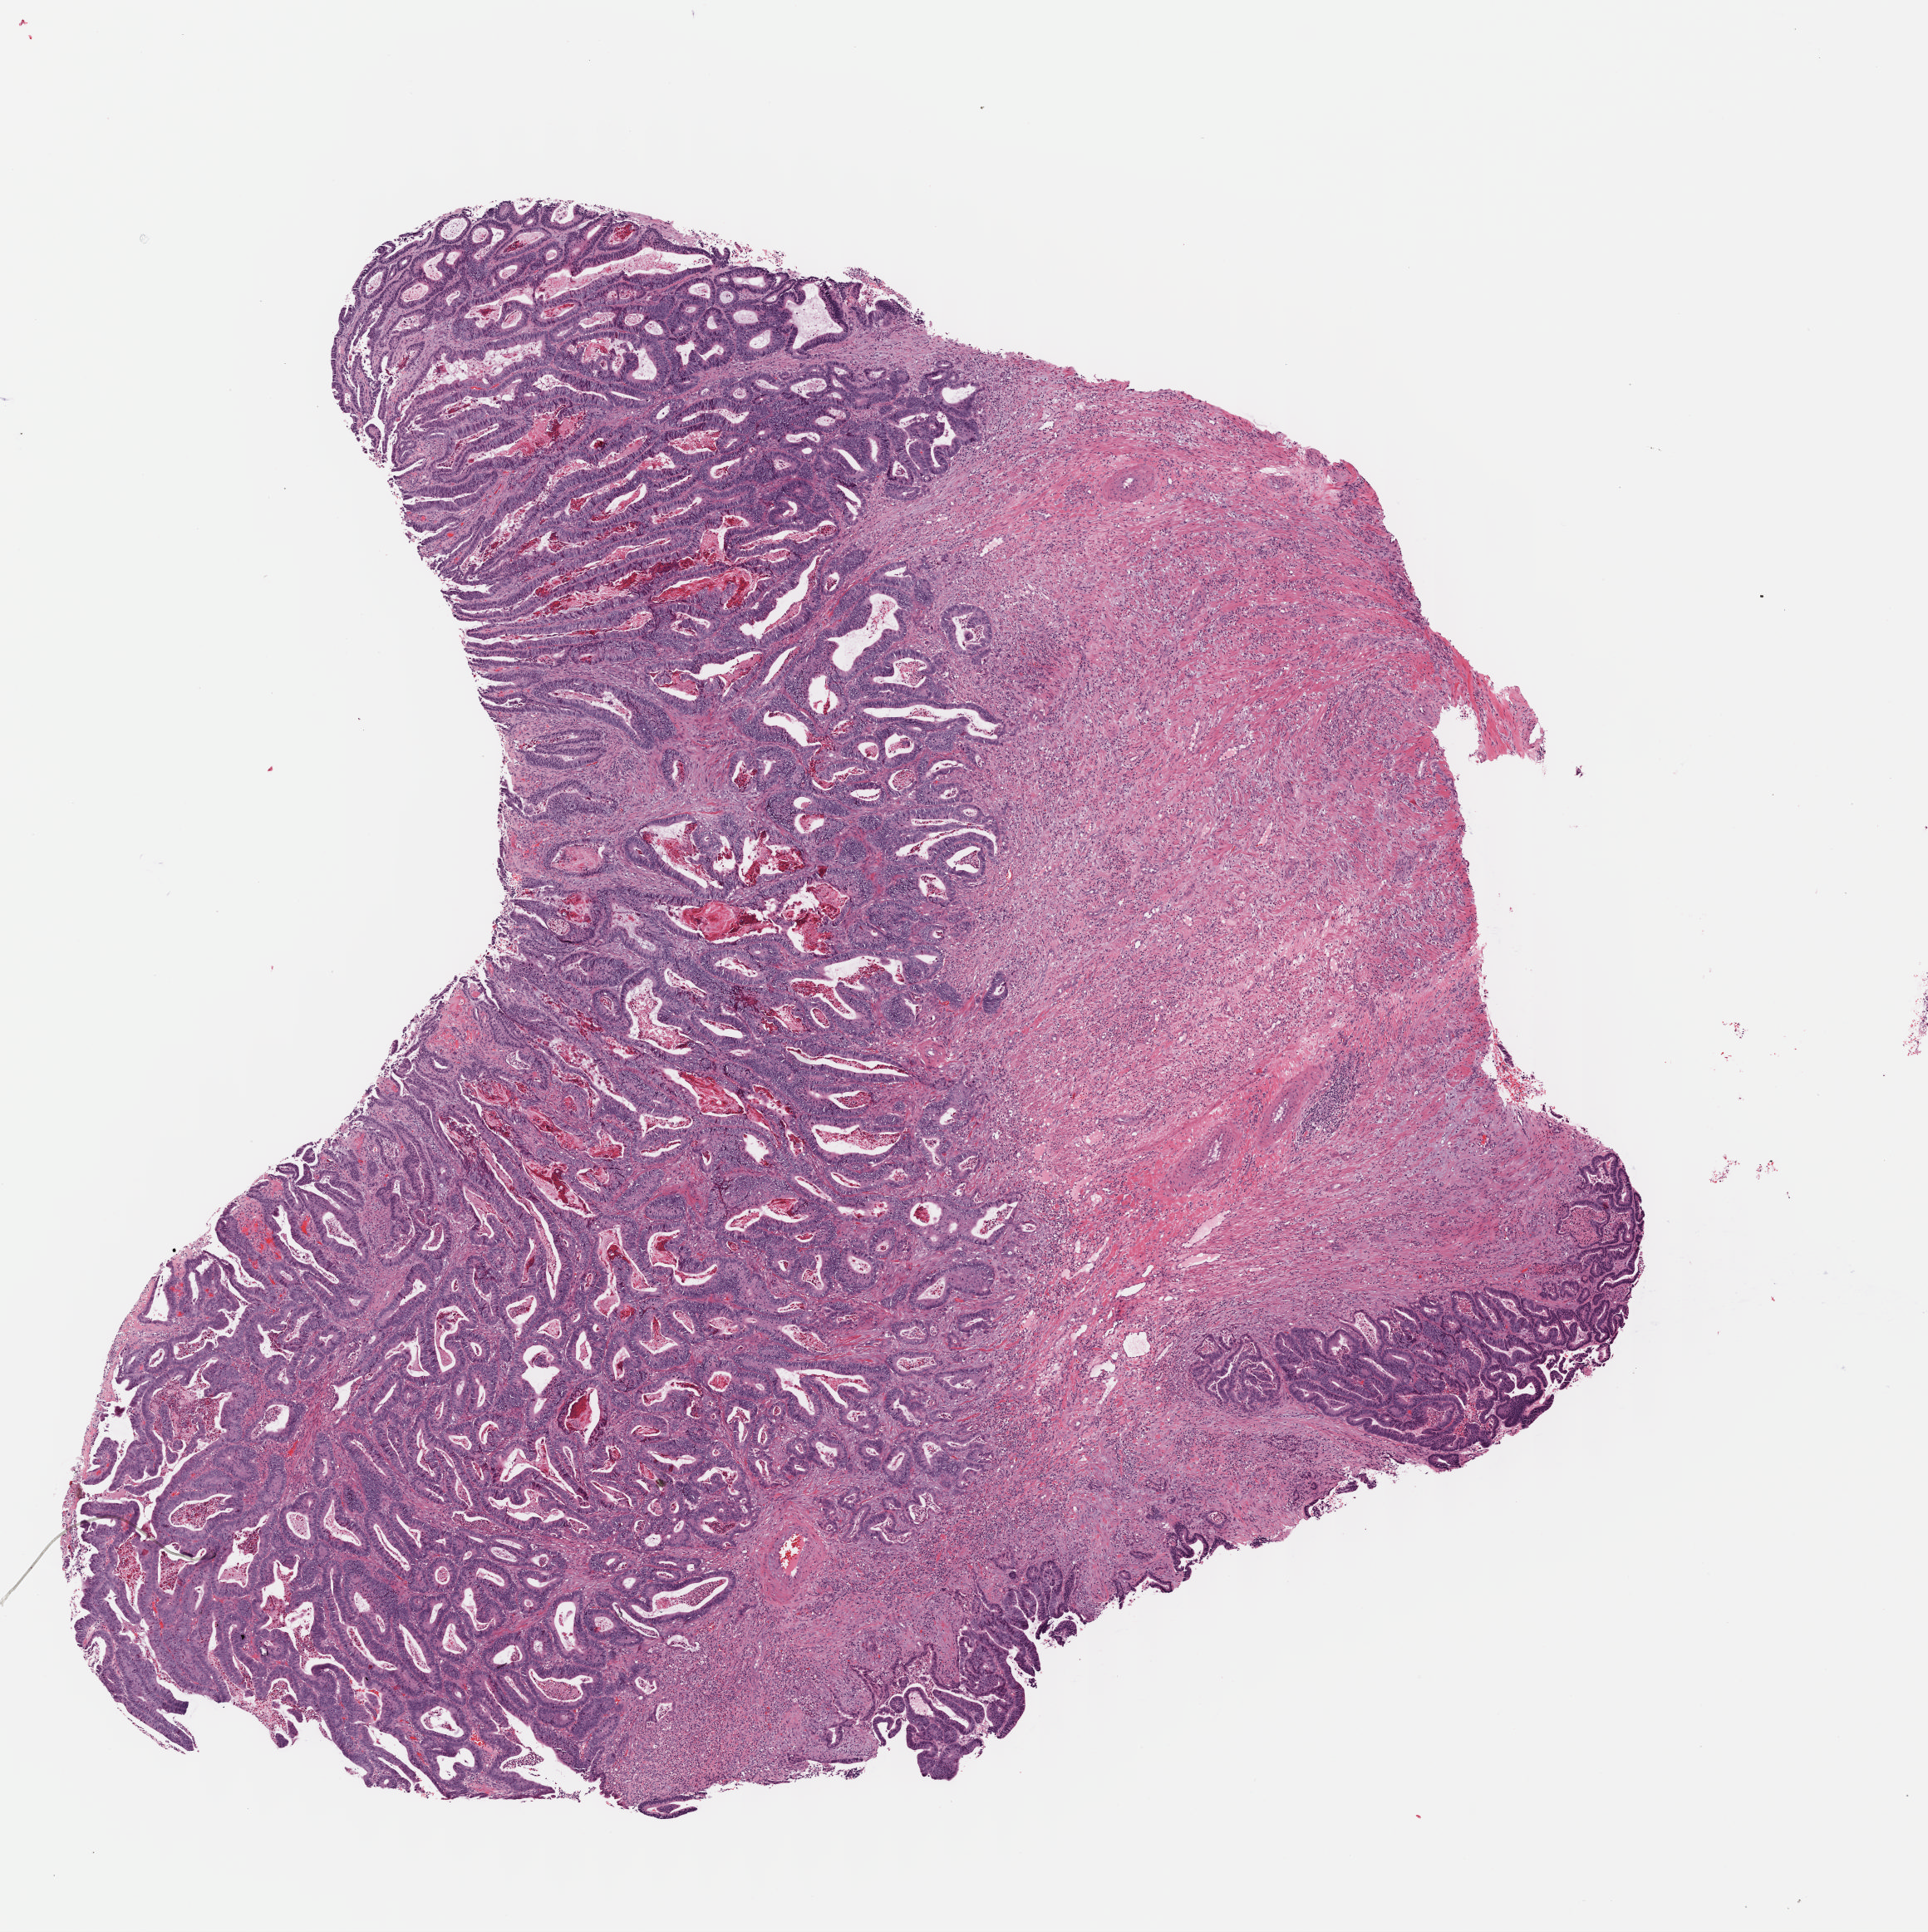
Digitized H&E tissue section (whole slide) — low-resolution overview of the scanned area, about 9.1 x 9.1 mm (slide scanned at 40x); frozen section from the bottom of the tissue portion; primary tumour sample from the colon. Male patient; age at initial diagnosis 62 years. Slide review estimates, as recorded: tumour cells 35%, tumour nuclei 65%, normal cells 0%, stromal cells 50%, necrosis 15%. Inflammatory infiltration, as recorded: lymphocyte infiltration 10%, monocyte infiltration 3%, neutrophil infiltration 10%.
- AJCC pathologic stage: IIA
- histologic diagnosis: Adenocarcinoma, NOS